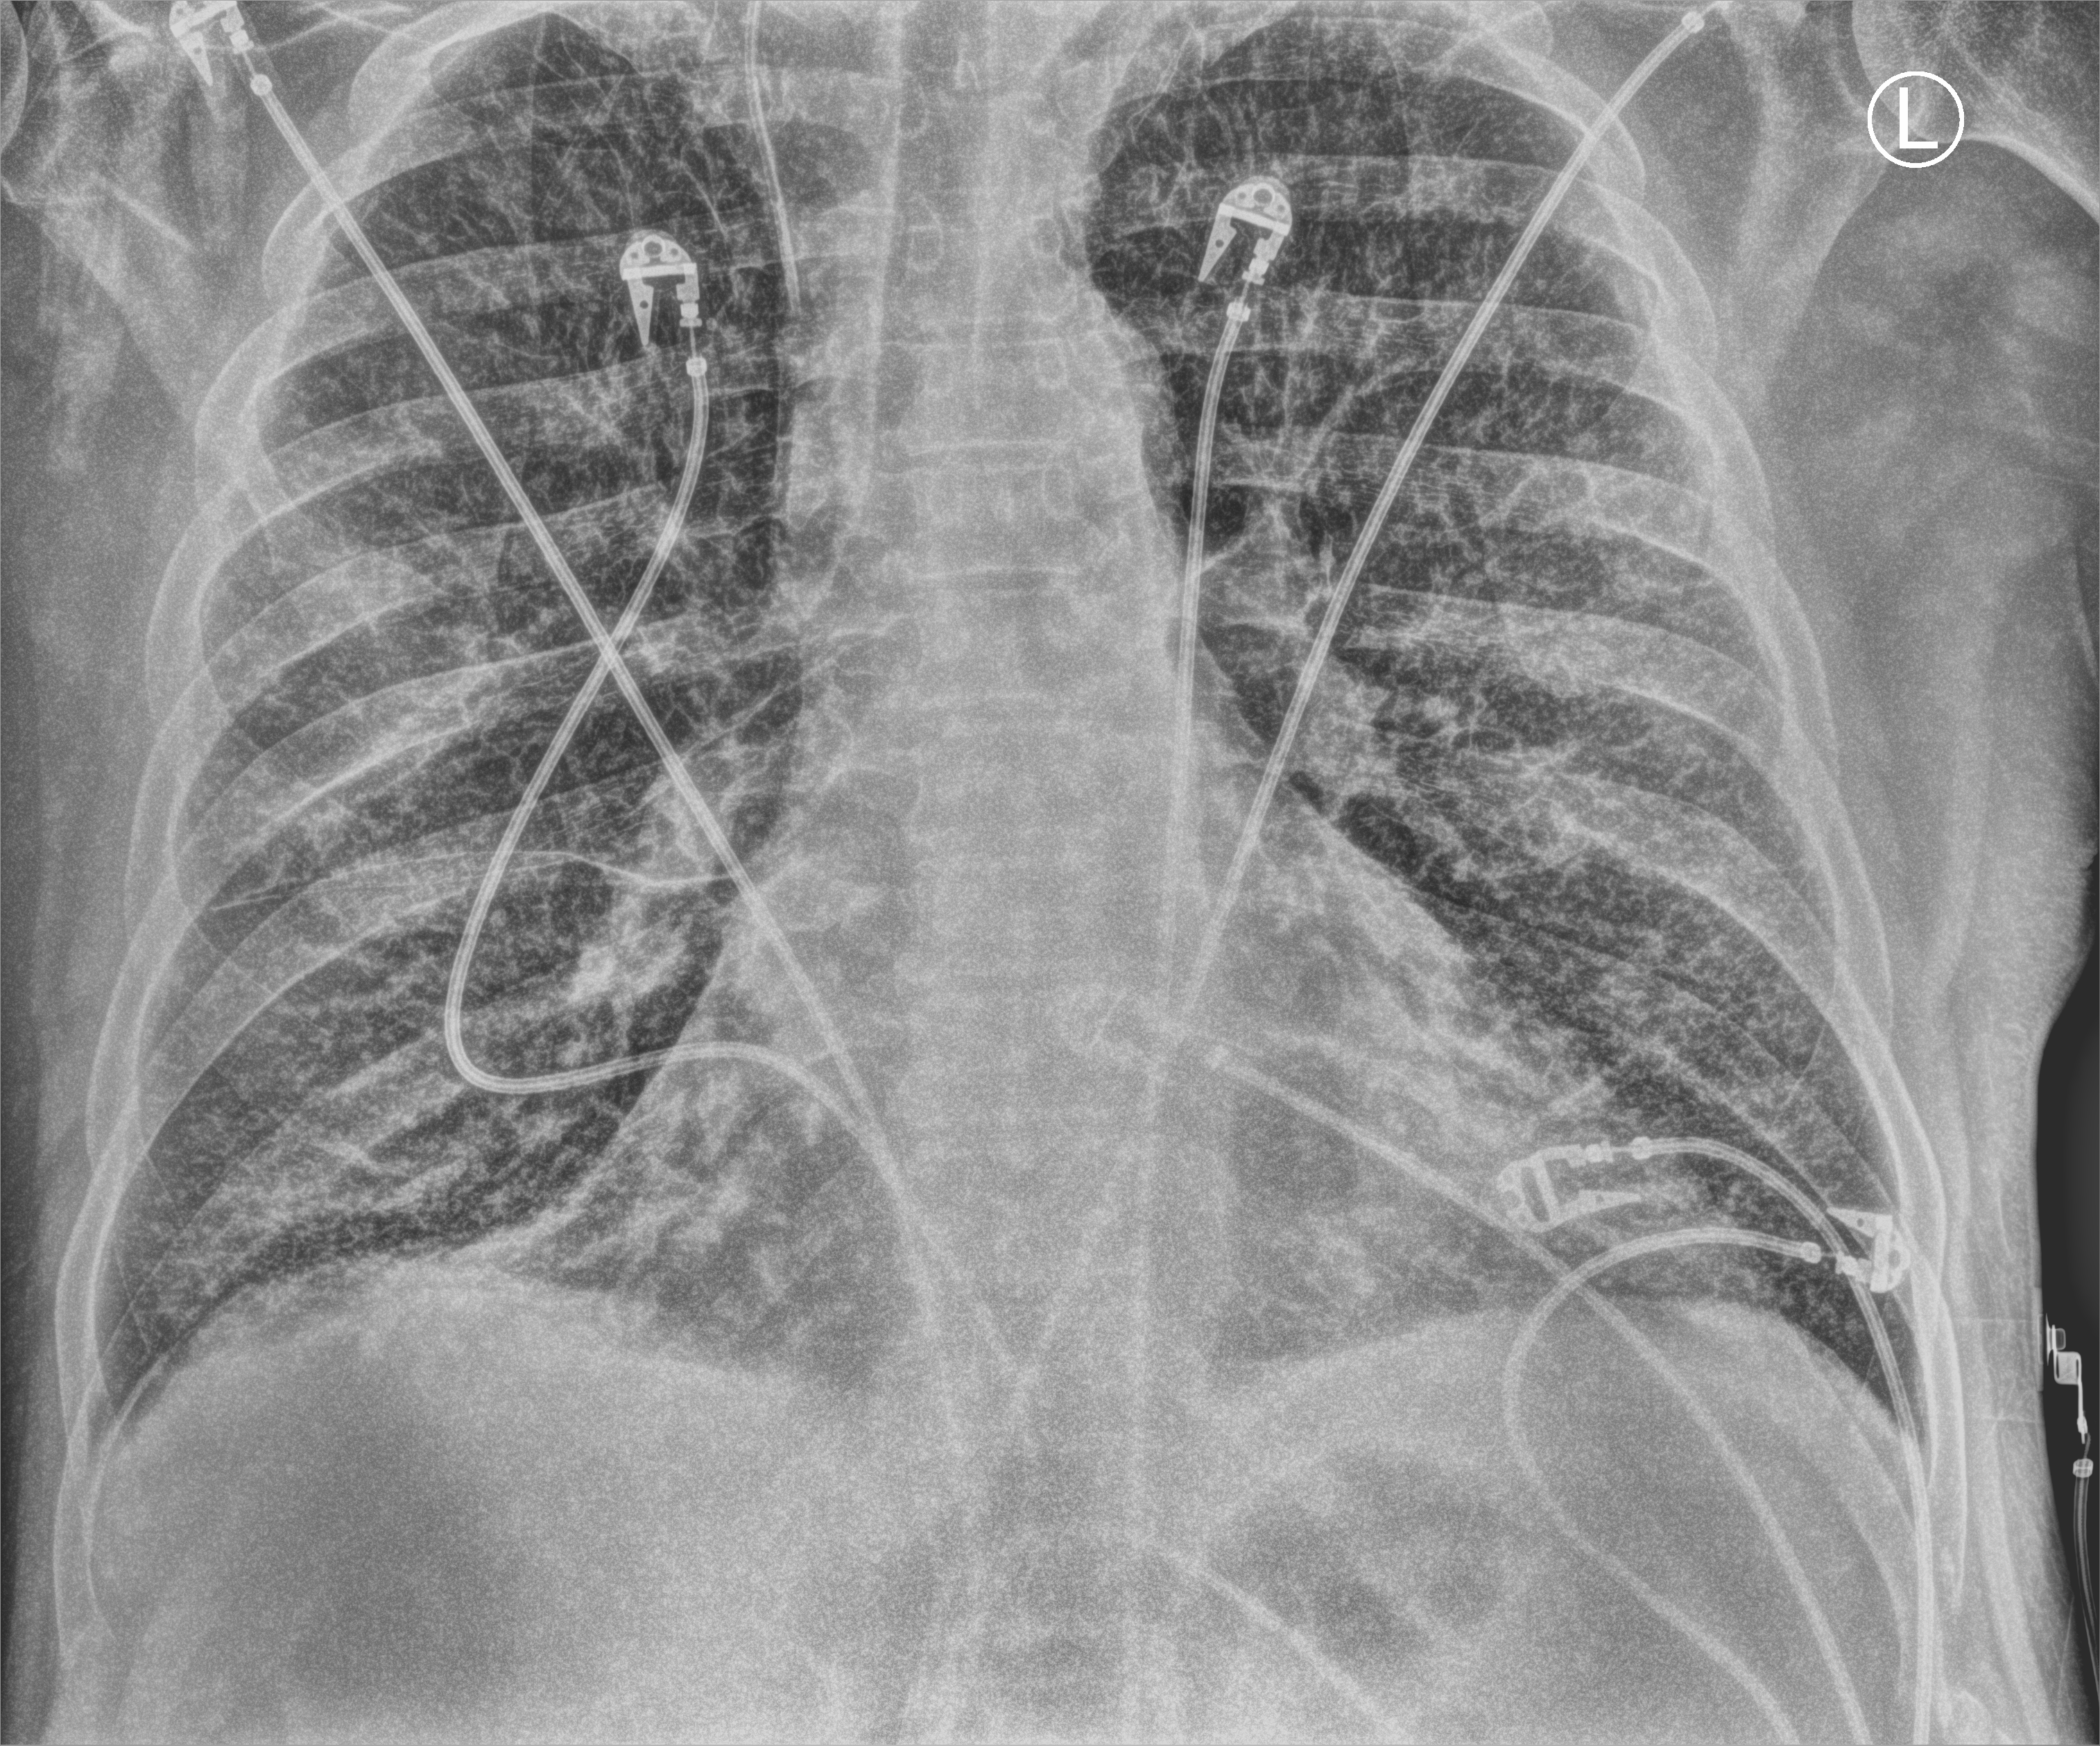
Portable chest radiograph. Adult patient hospitalised with COVID-19, age 18–59 years.
From the hospital-stay record, not from the radiograph (when in the stay this image was taken is not recorded):
- other chronic lung disease (admission record): yes